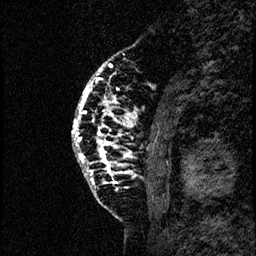
Breast MRI (dynamic contrast-enhanced), one sagittal slice. Position 18 of 60 along the scan axis. Dynamic contrast-enhanced study with each time point stored as its own series, time point 2 of 4 at this slice position (early post-contrast, ordered by acquisition time). 1.5 T. TE 4.2 ms, TR 17.6 ms. 2 mm slice thickness. 256 × 256 image matrix. Female patient, age 40 years. Case-level facts recorded for this patient, not image findings: setting: breast cancer imaged before/during neoadjuvant chemotherapy; receptor status: HER2-positive.
Structures marked on this image (semi-automatically segmented with operator editing):
- analysis volume of interest (the breast-tissue region the enhancement analysis was run in; not a lesion): bounding box <68,55,185,206> (left, top, right, bottom; pixels)
- tumour enhancement mask (voxels above the 100 % enhancement threshold inside the analysis volume of interest): <71,63,156,175>